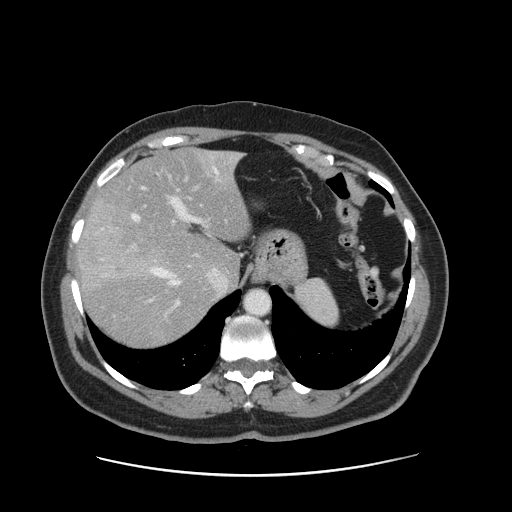
Contrast-enhanced abdominal CT, one axial slice; position 114 of 161 along the scan axis; 120 kVp; intravenous contrast given; soft-tissue window (W 400 / L 40 HU); 2.5 mm slice thickness; 512 × 512 image matrix, field of view 398 × 398 mm. Female patient, age 62 years. Case-level facts recorded for this patient, not image findings: diagnosis: colorectal cancer liver metastases, imaged before liver resection; multiple liver metastases: no; largest metastasis: 2.5 cm; disease in both lobes: no.
Outlined on this slice (outlined manually by an expert reader):
- hepatic veins: bounding box (x1, y1, x2, y2) in pixels: (133, 155, 240, 288)
- liver: (79, 149, 251, 349)
- planned liver remnant (the part of the liver to remain after resection): (96, 149, 251, 283)
- portal vein (with intrahepatic branches): (162, 170, 207, 306)
- liver metastasis: (117, 266, 122, 272)